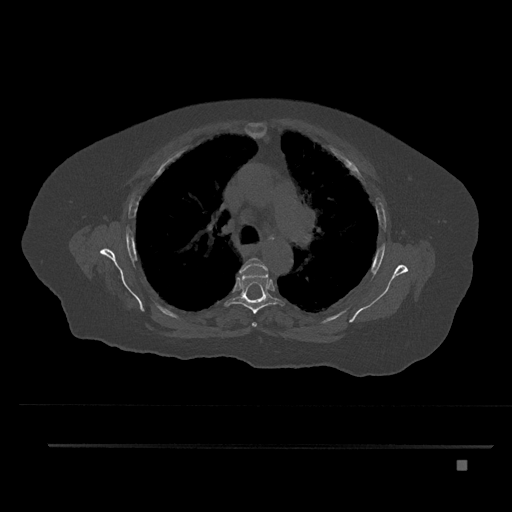
CT including the spine, one axial slice. Position 573 of 797 along the scan axis. 120 kVp. Bone window (W 1800 / L 400 HU). 512 × 512 image matrix, field of view 437 × 437 mm. Patient: female, 76 years. From the clinical record (not read from this slice): primary cancer: lung; vertebrae with lytic lesions (as recorded): T11, L3.
Outlined on this slice (semi-automatically segmented with operator editing):
- T4 vertebra: bounding box <240,258,268,327> (left, top, right, bottom; pixels)
- T5 vertebra: <224,274,285,314>